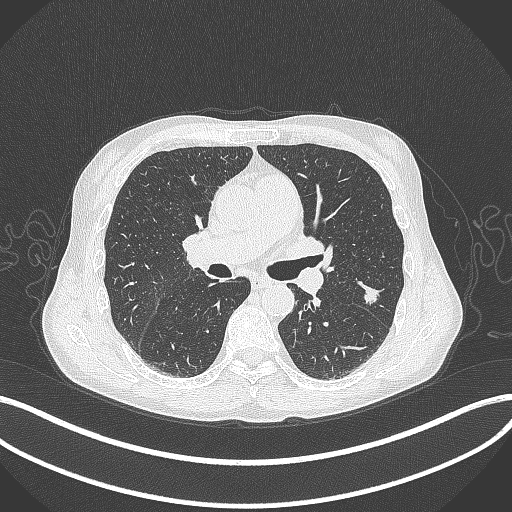
Chest CT, one axial slice; position 210 of 429 along the scan axis; reconstruction kernel B70f; 120 kVp; lung window (W 1500 / L -600 HU); 1 mm slice thickness; 512 × 512 image matrix, field of view 400 × 400 mm. Male patient, age 58 years. Case-level facts recorded for this patient, not image findings: clinical TNM (as recorded): T1c N0 M0.
Structures marked on this image (bounding box drawn by a radiologist):
- lung tumour (recorded histology: adenocarcinoma): box from (x=361, y=283) to (x=381, y=307) px